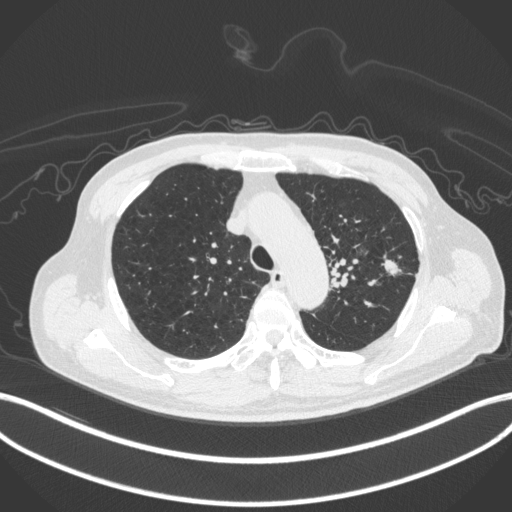
Chest CT, one axial slice. Position 332 of 420 along the scan axis. 120 kVp. Lung window (W 1500 / L -600 HU). 1 mm slice thickness. 512 × 512 image matrix. Patient: male, 77 years. From the clinical record (not read from this slice): clinical TNM (as recorded): T3 N1 M0.
Outlined on this slice (rectangle marked by the reading radiologist):
- lung tumour (recorded histology: adenocarcinoma): bounding box (x1, y1, x2, y2) in pixels: (382, 257, 404, 276)